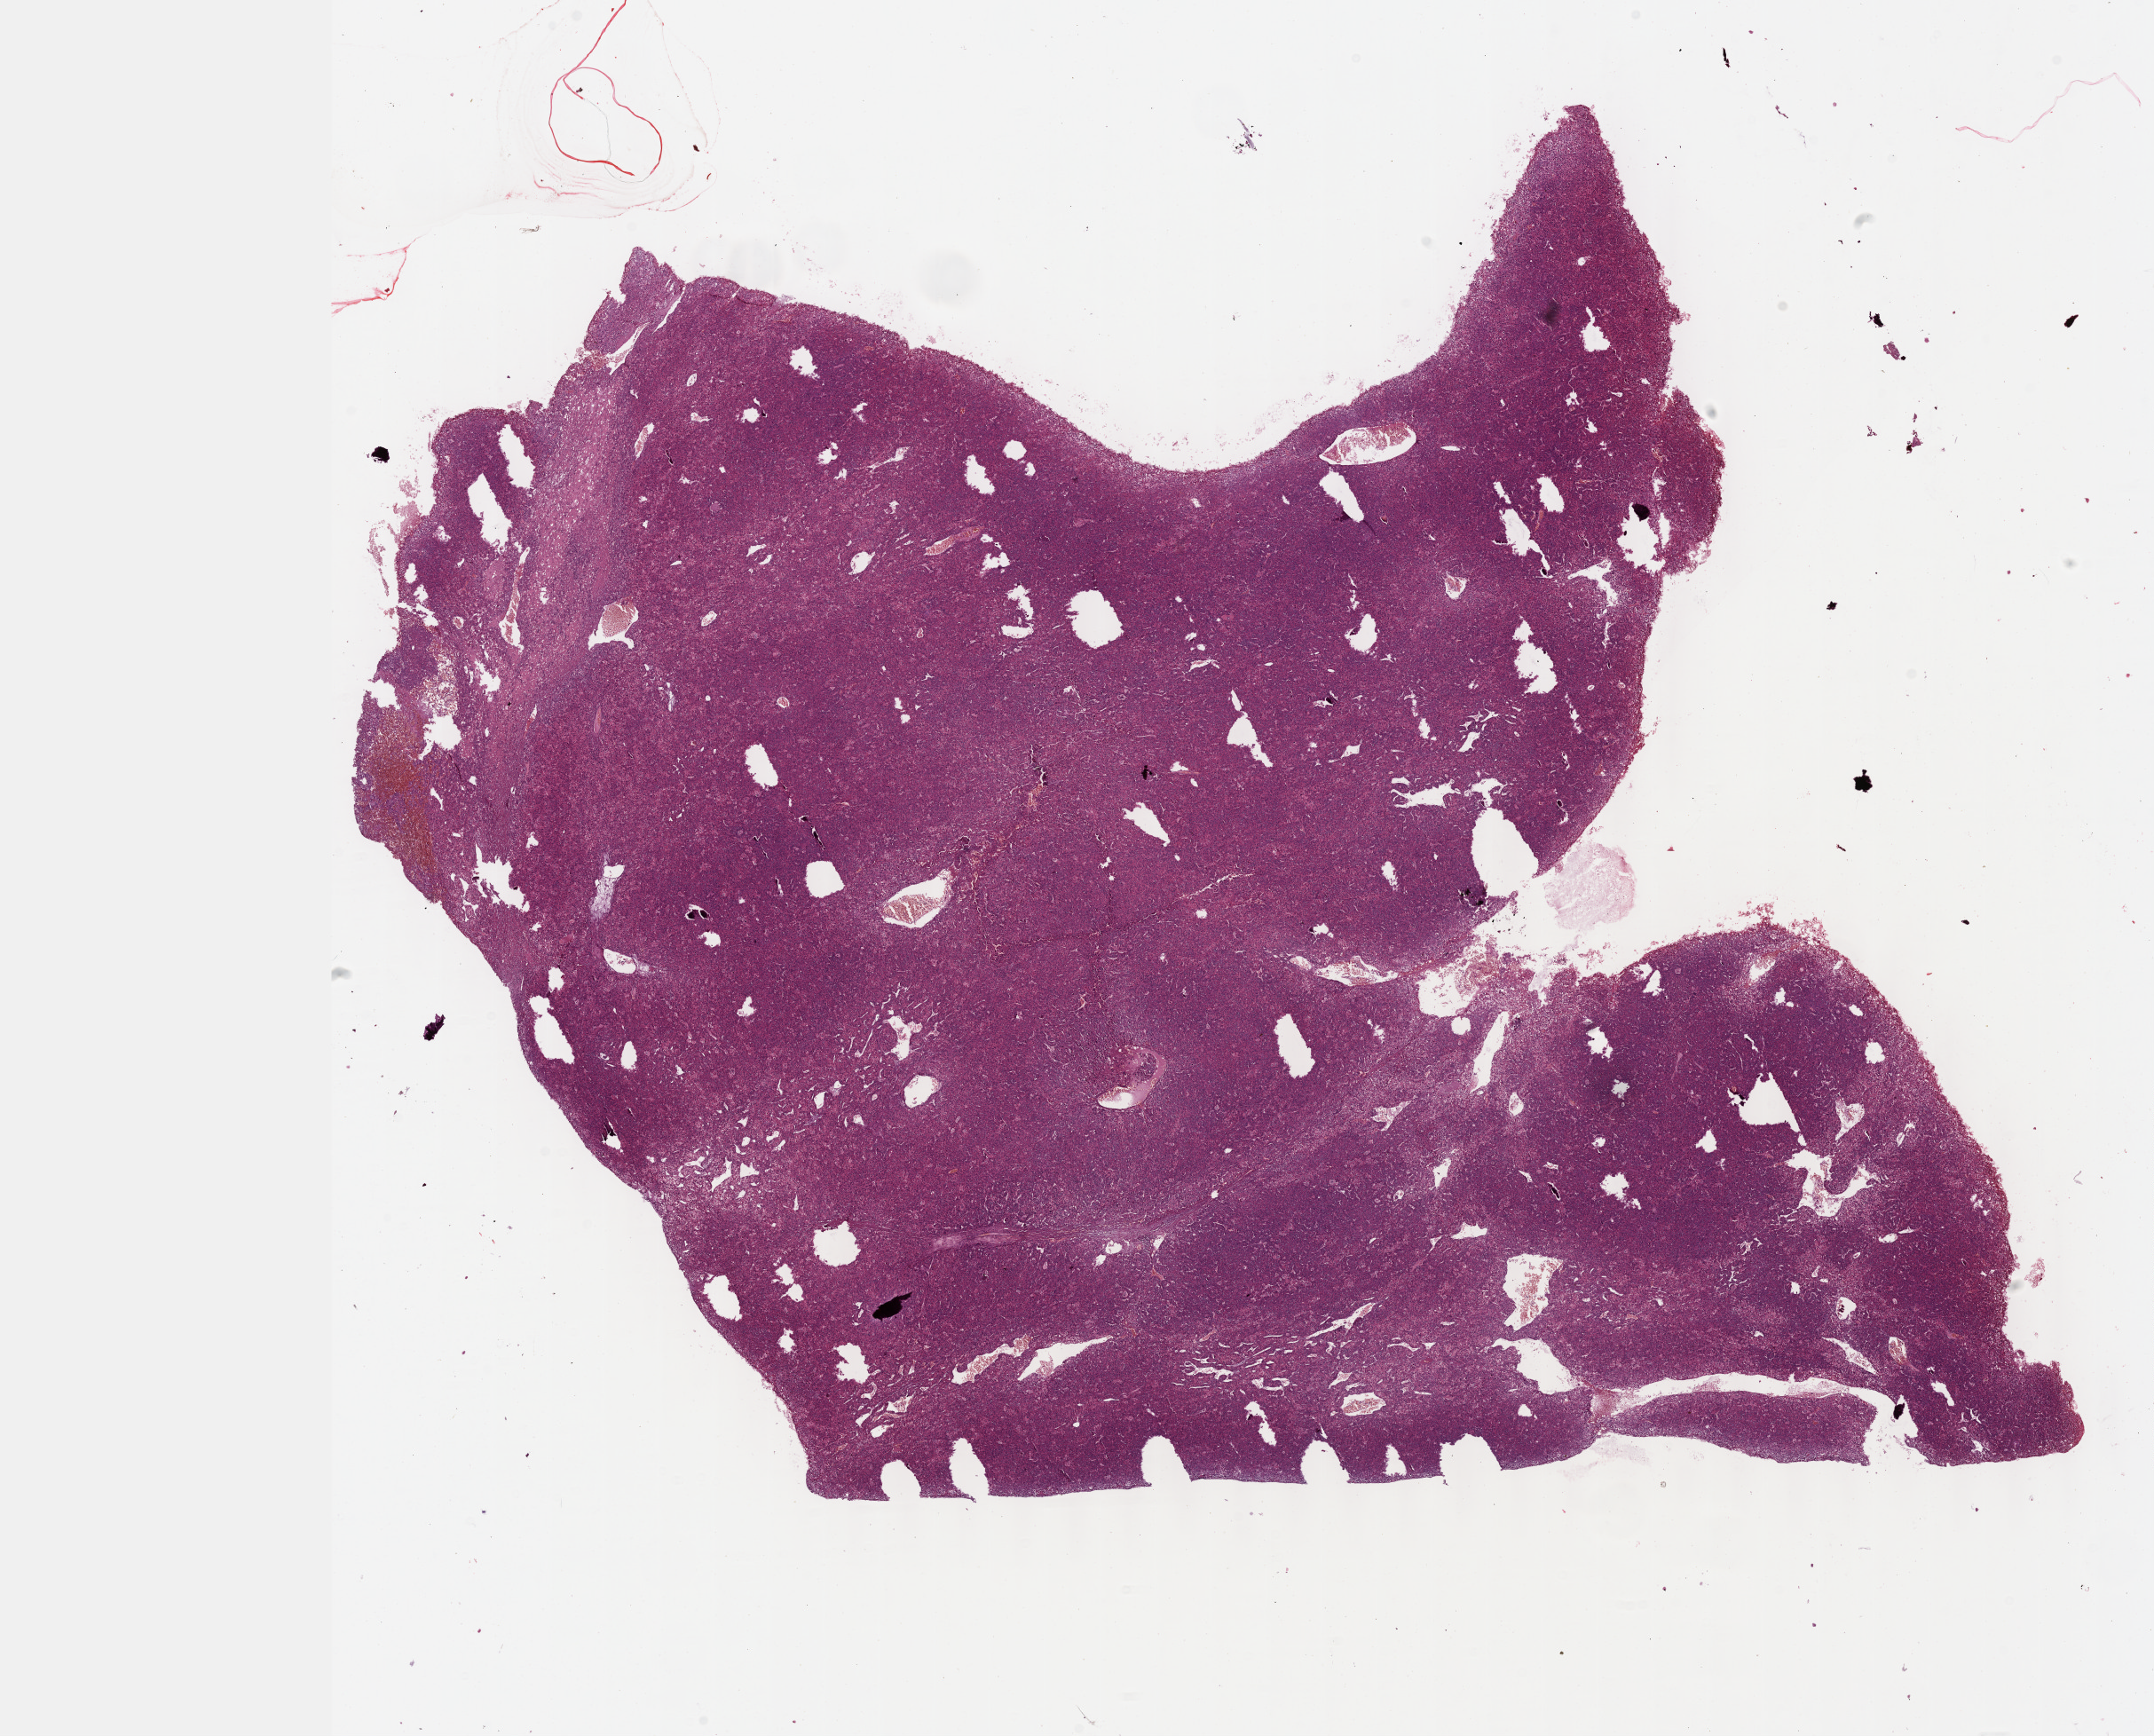
Digitized H&E-stained tissue section (whole slide) — a low-resolution overview of the entire scanned area, about 19.6 x 15.8 mm (acquisition: 40x scan). Formalin-fixed paraffin-embedded (FFPE) diagnostic section. Sample: primary tumour, liver. Male patient; age at initial diagnosis 59 years. Histologic grade: G3 (poorly differentiated).
- TNM: T3 N0 M0
- histologic diagnosis: Hepatocellular carcinoma, NOS
- AJCC pathologic stage: IIIA